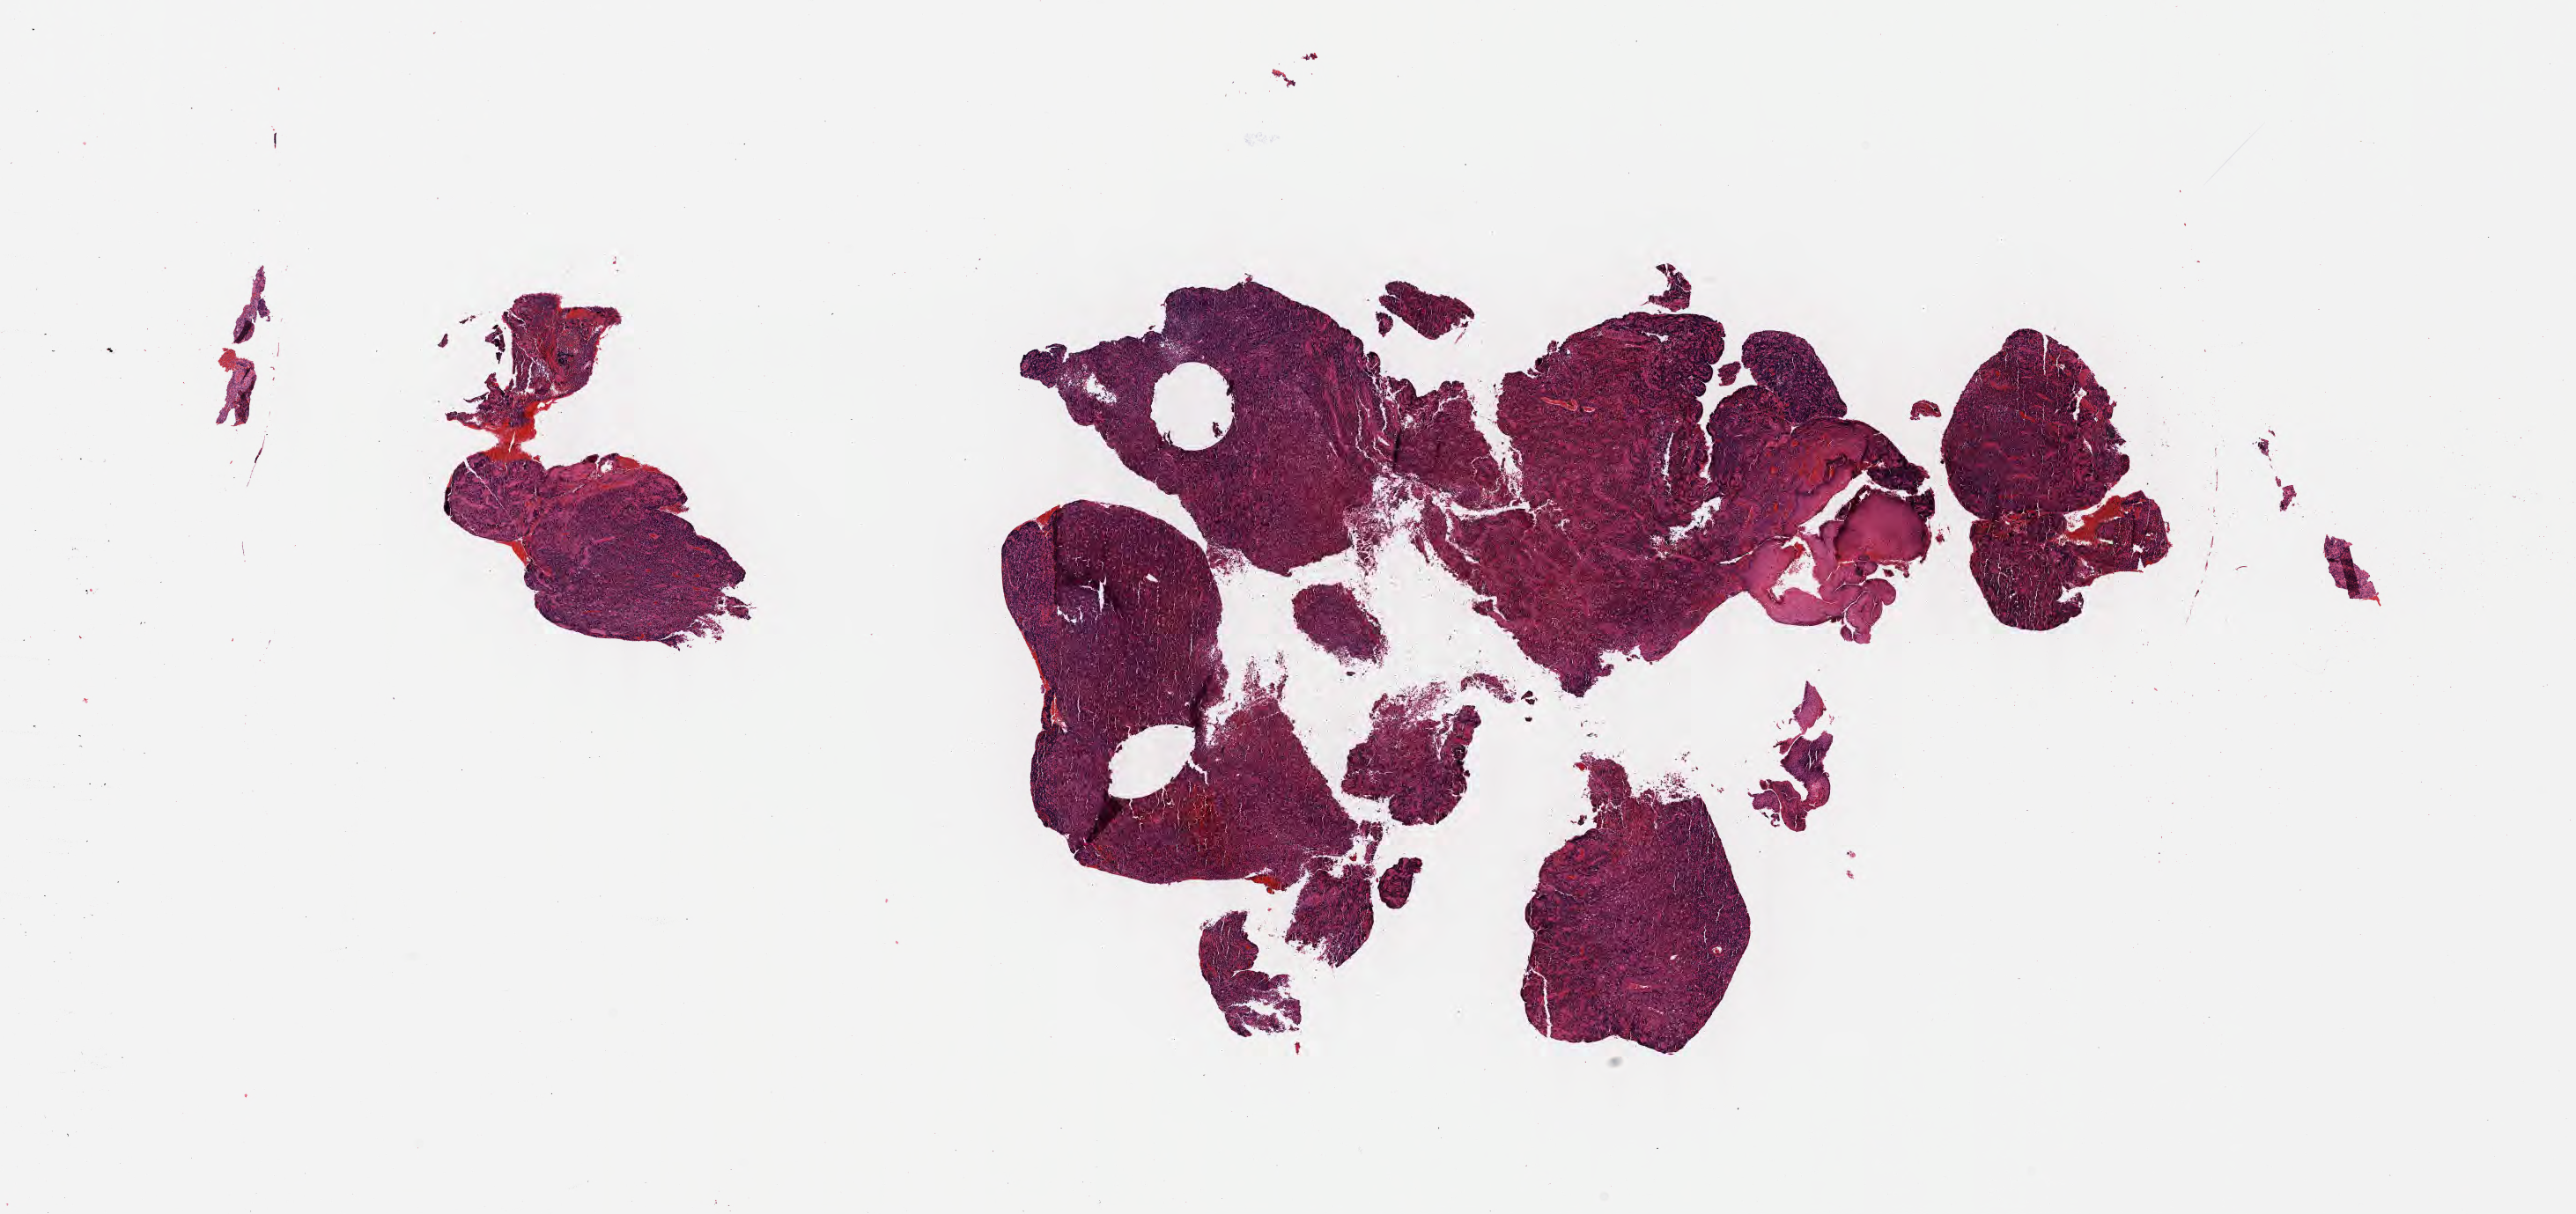
Digitized haematoxylin and eosin-stained section — low-resolution overview of the scanned area, about 23.6 x 11.1 mm; formalin-fixed paraffin-embedded section; specimen: primary tumor; anatomic site: cranium. Patient: male, age at initial diagnosis 5 years. Composition of this section per pathologist review: tumor cells 80%, tumor nuclei 80%, stromal cells 10%, necrosis 5%, normal cells 5%. Inflammatory infiltration, as recorded: lymphocyte infiltration 30%, monocyte infiltration 30%, neutrophil infiltration 5%.
Diagnosis: Burkitt lymphoma, NOS. Ann Arbor stage (patient): Stage II.